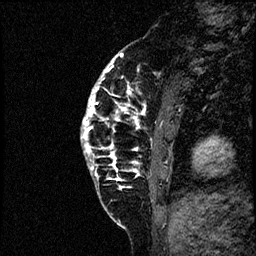
Breast MRI (dynamic contrast-enhanced), one sagittal slice; dynamic contrast-enhanced study with each time point stored as its own series, time point 2 of 4 at this slice position (early post-contrast, ordered by acquisition time); 1.5 T; TE 4.2 ms, TR 17.6 ms; 2 mm slice thickness; 256 × 256 image matrix, field of view 200 × 200 mm. Female patient, age 40 years. From the clinical record (not read from this slice): setting: breast cancer imaged before/during neoadjuvant chemotherapy; receptor status: HER2-positive.
Annotated regions visible in this slice (semi-automatically segmented with operator editing):
- analysis volume of interest (the breast-tissue region the enhancement analysis was run in; not a lesion): bounding box (x1, y1, x2, y2) in pixels: (82, 56, 197, 205)
- tumour enhancement mask (voxels above the 100 % enhancement threshold inside the analysis volume of interest): (82, 56, 146, 181)